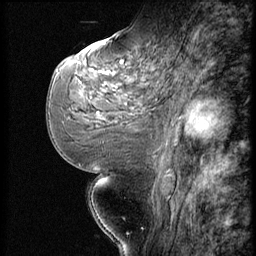
Breast MRI (dynamic contrast-enhanced), one sagittal slice; slice 27 of 56 in the series (ordered by position); dynamic contrast-enhanced series, image 2 of 3 at this slice position (ordered by acquisition); 1.5 T; TE 4.2 ms, TR 9 ms; 2.5 mm slice thickness; 256 × 256 image matrix, field of view 180 × 180 mm. Patient: female, 51 years. Case-level facts recorded for this patient, not image findings: setting: breast cancer imaged before/during neoadjuvant chemotherapy; receptor status: triple-negative.
Annotated regions visible in this slice (semi-automatic segmentation, software-assisted and operator-edited):
- analysis volume of interest (the breast-tissue region the enhancement analysis was run in; not a lesion): bounding box (x1, y1, x2, y2) in pixels: (73, 46, 172, 147)
- tumour enhancement mask (voxels above the 140 % enhancement threshold inside the analysis volume of interest): (107, 72, 111, 75)